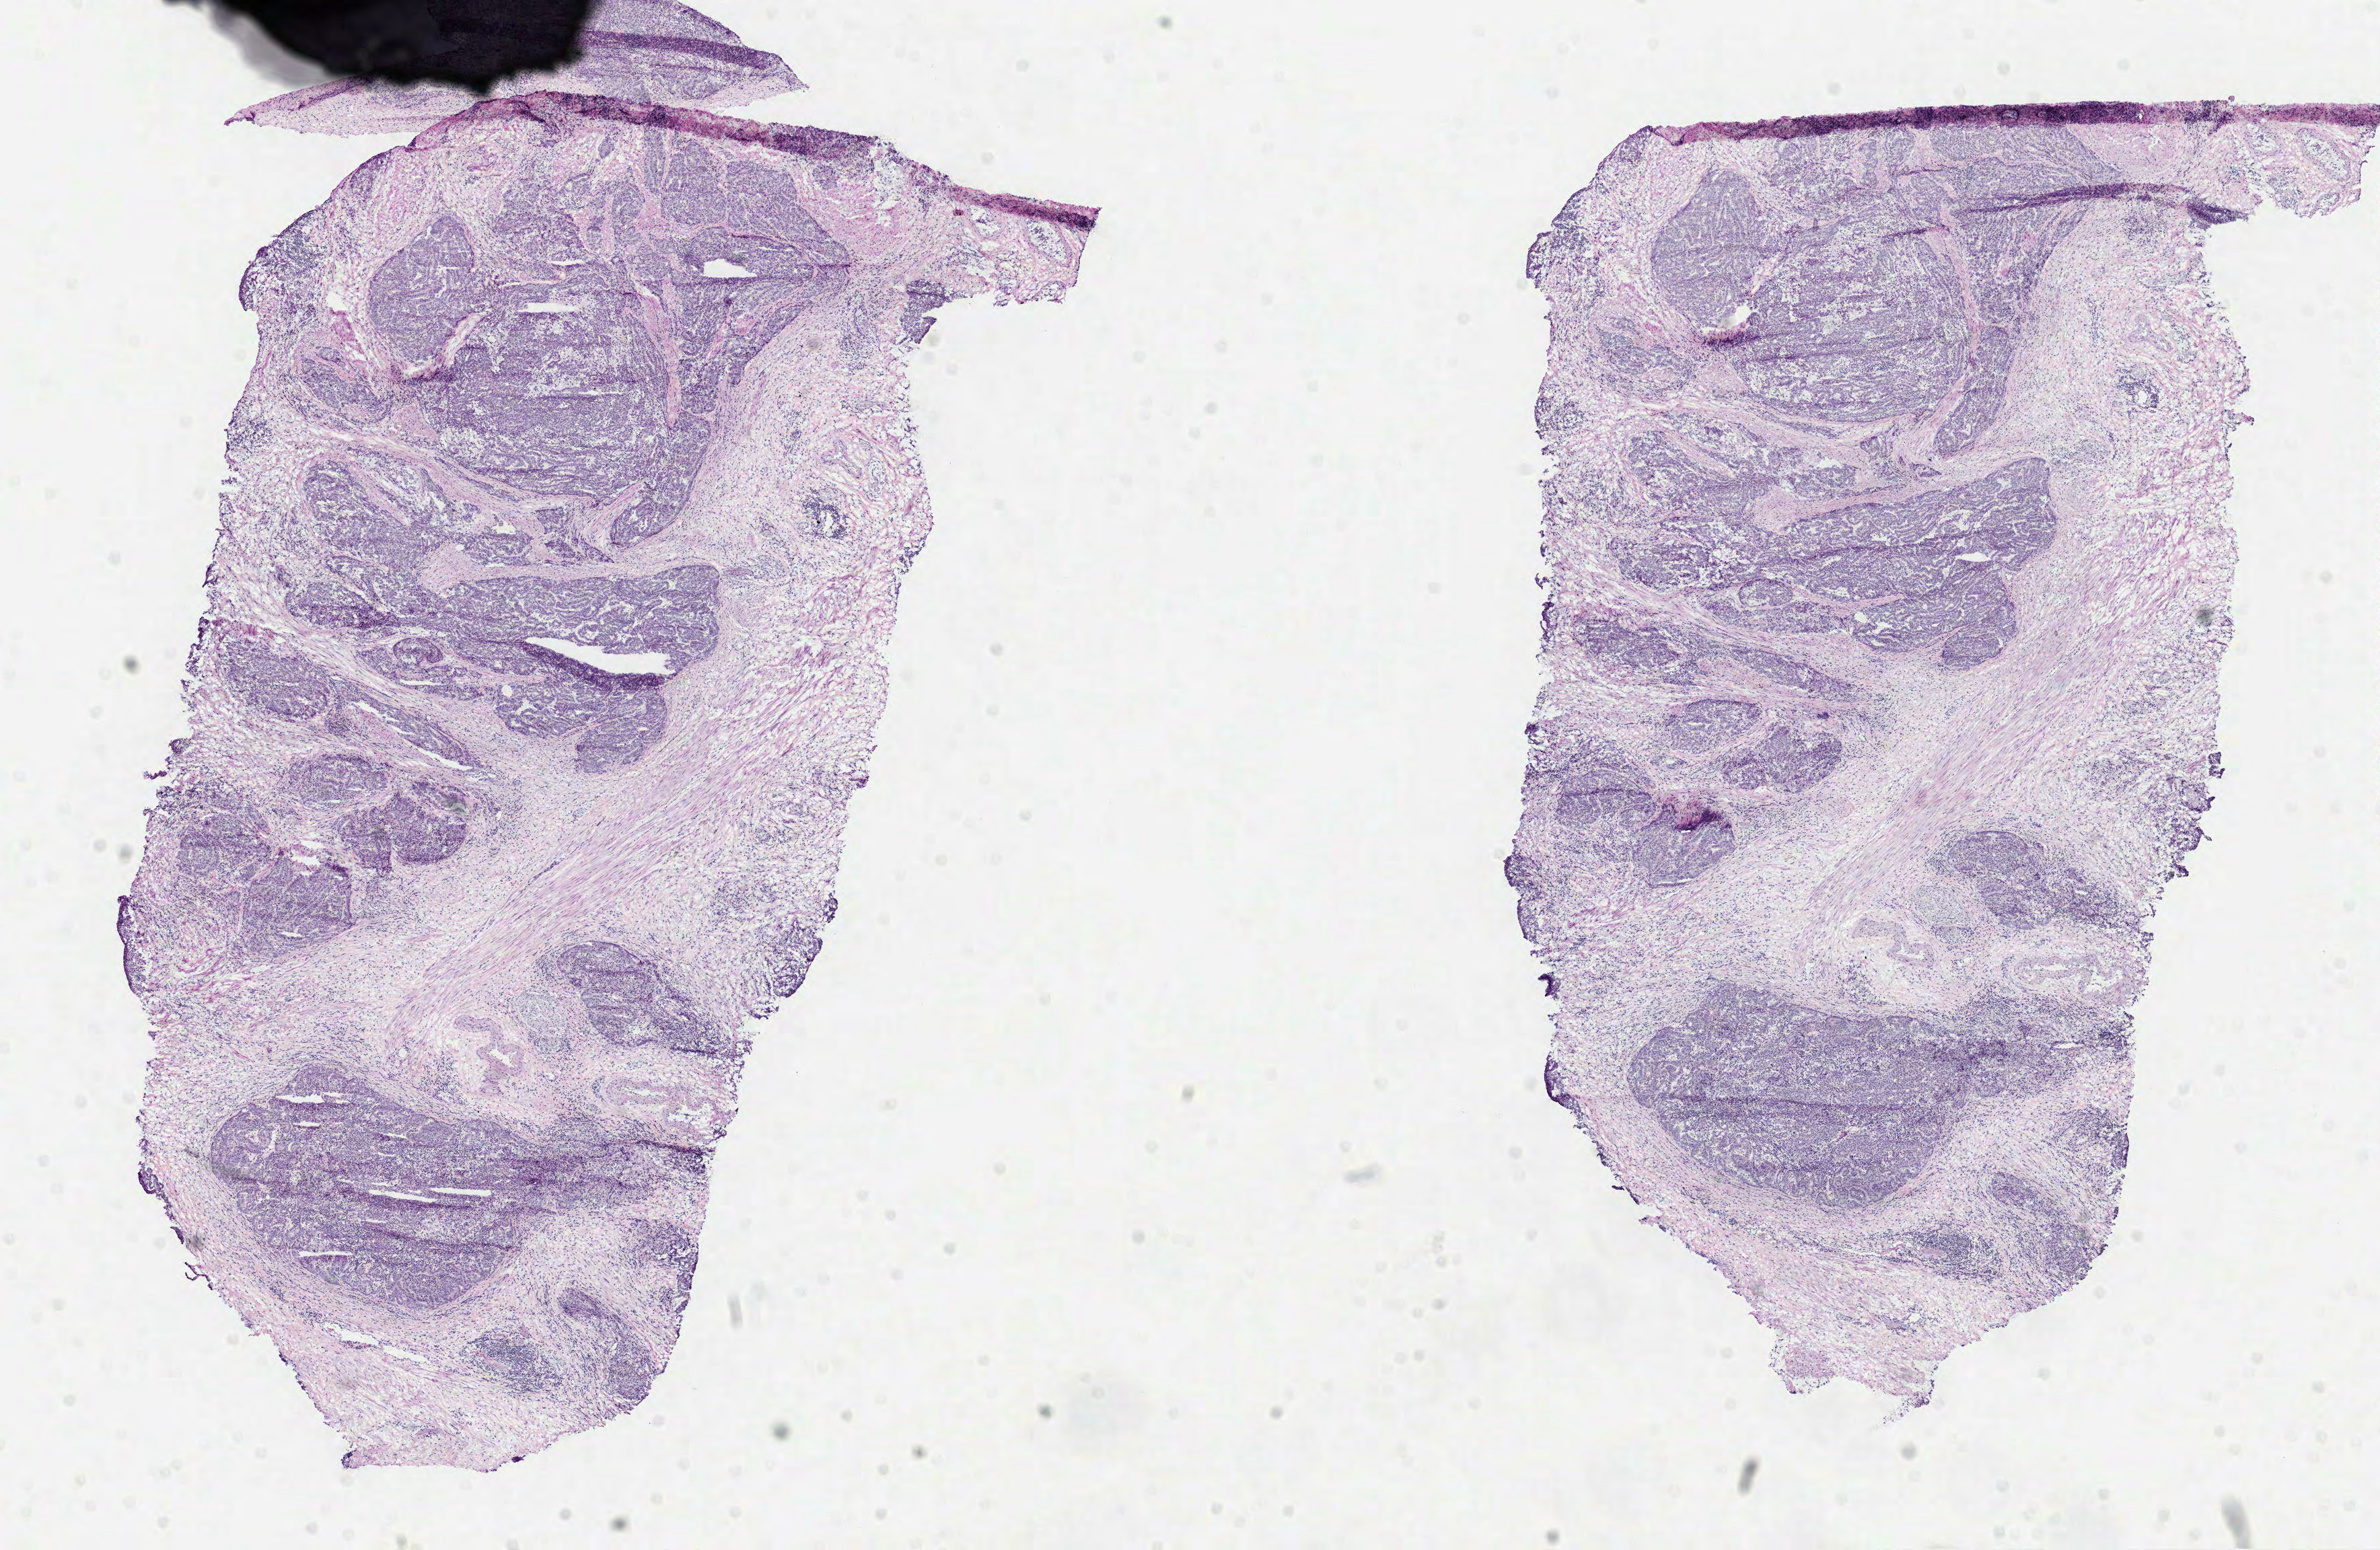
Whole-slide histology image, Hematoxylin and eosin (H&E) stained, shown as a low-resolution overview of the whole scanned area (about 14.3 x 9.3 mm), FFPE section, sample: primary tumour, prostate. Patient: male, age at initial diagnosis 70 years. Gleason score: 9 (4+5).
* diagnosis: Acinar cell carcinoma (prostate gland)
* lymph nodes positive (case pathology): 3 of 10 examined